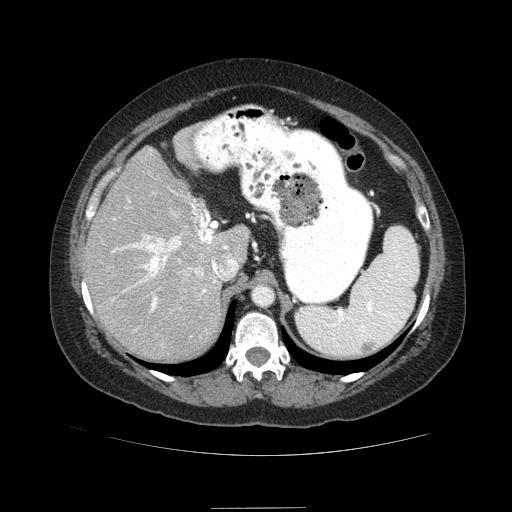
Contrast-enhanced abdominal CT (liver protocol), one axial slice; position 58 of 89 along the scan axis; reconstruction kernel STANDARD; 120 kVp; soft-tissue window (W 400 / L 40 HU); 2.5 mm slice thickness; 512 × 512 image matrix, field of view 400 × 400 mm. Case-level facts recorded for this patient, not image findings: diagnosis: hepatocellular carcinoma (patient treated with transarterial chemoembolisation; whether this scan precedes or follows treatment is not stated here); TNM stage (as recorded): Stage-IIIB; Child-Pugh class: A.
Structures marked on this image (semi-automatically segmented with operator editing):
- abdominal aorta: box from (x=254, y=284) to (x=273, y=305) px
- liver parenchyma outside the tumour (the mass and vessels are separate outlines, so this box may not span the whole liver): (x=82, y=126)–(x=250, y=360)
- liver vessels: (x=112, y=190)–(x=228, y=312)